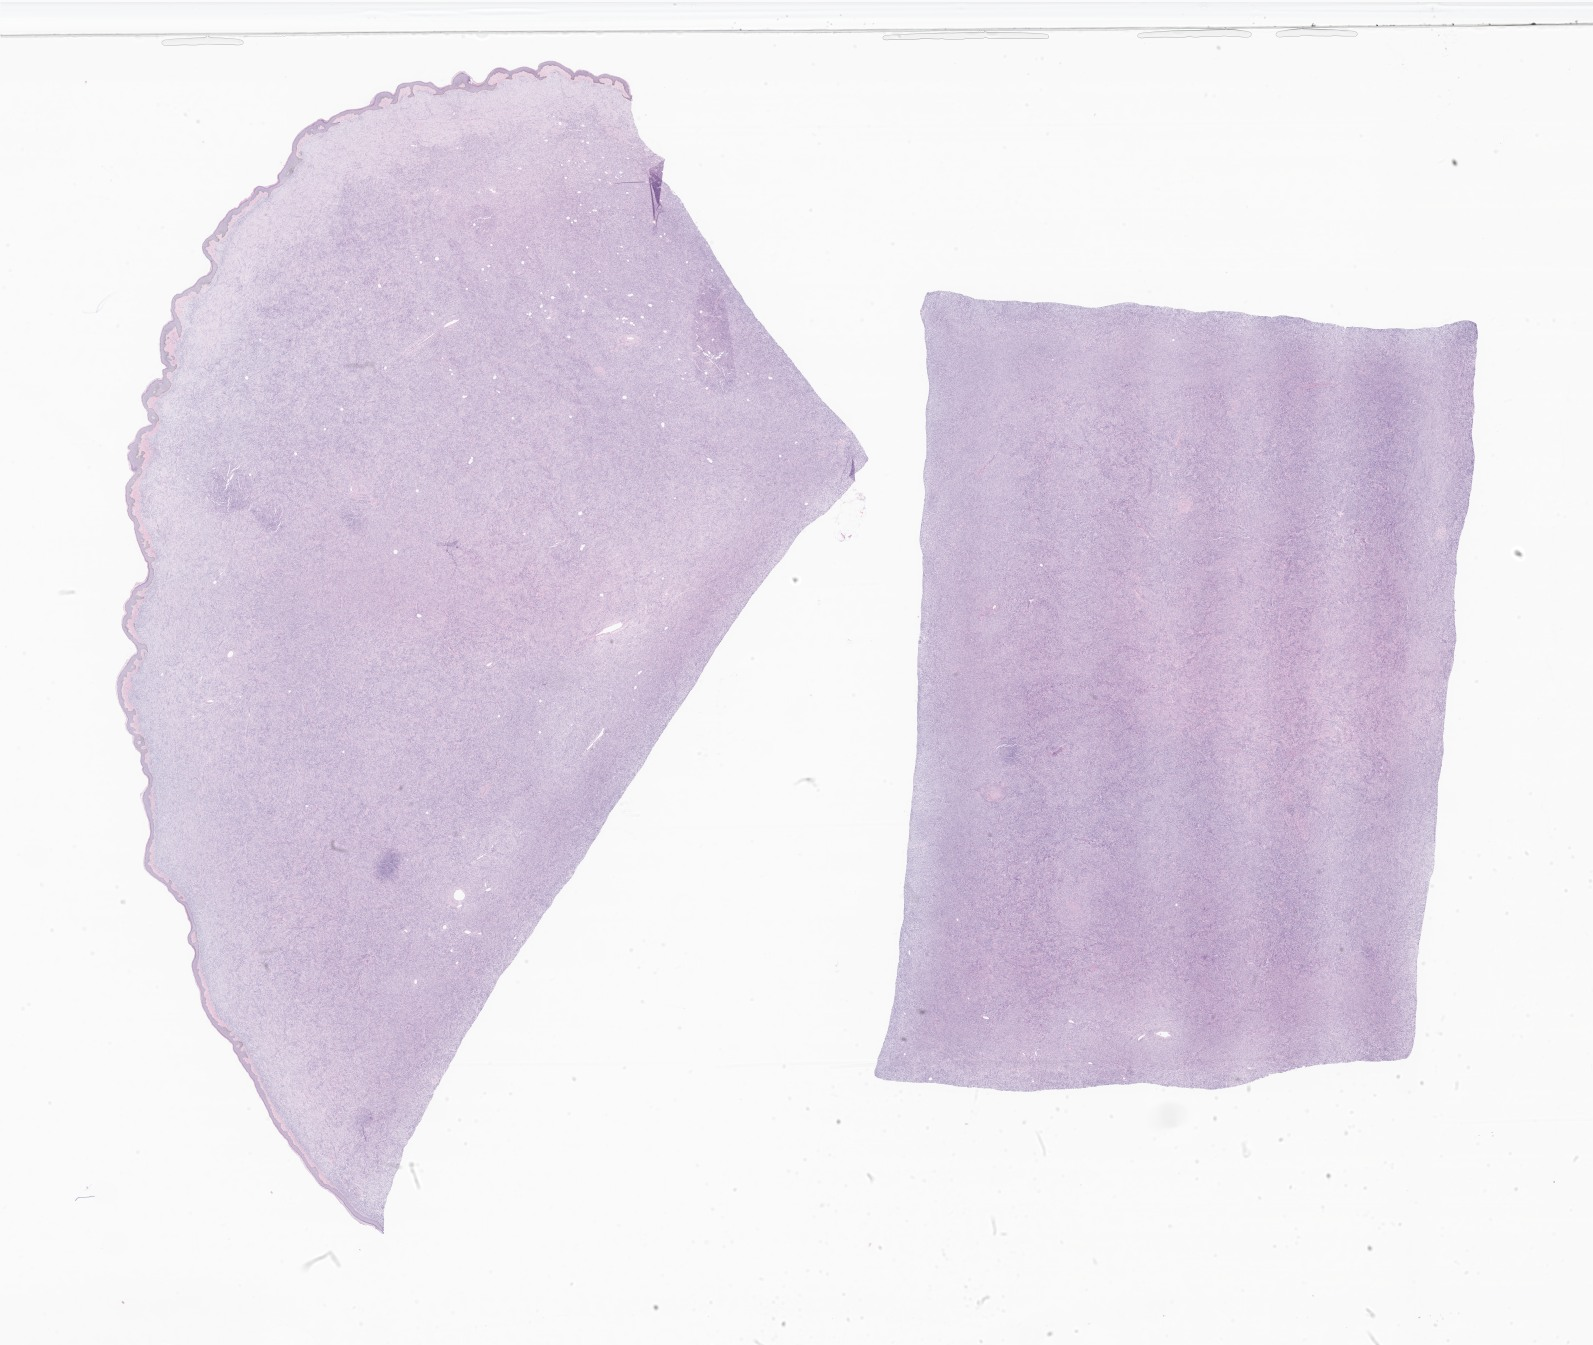
Digitized haematoxylin and eosin-stained section of tumor tissue from the abdomen, low-resolution overview of the scanned area, about 26.9 x 22.7 mm. FFPE section. Female patient, age 143 months.
- recorded diagnosis: Pigmented dermatofibrosarcoma protuberans